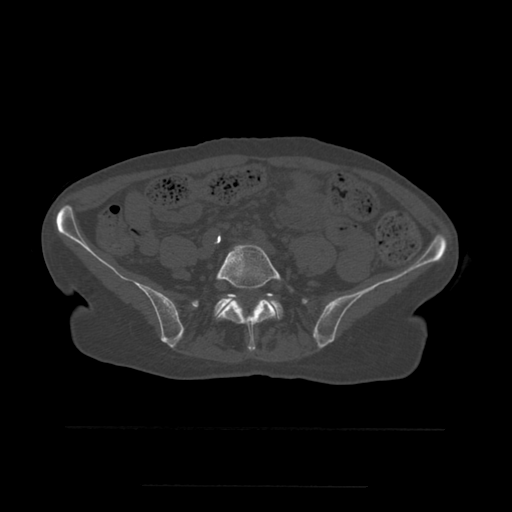
CT including the spine, one axial slice. Position 142 of 544 along the scan axis. Bone window (W 1800 / L 400 HU). 1.25 mm slice thickness. 512 × 512 image matrix. Patient age 58 years. From the clinical record (not read from this slice): primary cancer: lung.
Outlined on this slice (semi-automatically segmented with operator editing):
- L5 vertebra: bounding box <216,245,293,352> (left, top, right, bottom; pixels)